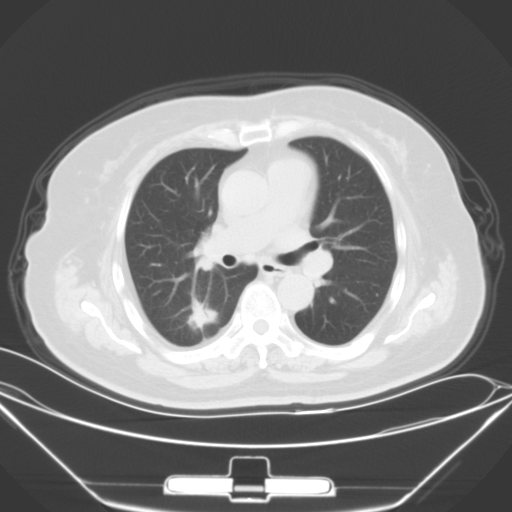
Chest CT, one axial slice; position 37 of 64 along the scan axis; 120 kVp; lung window (W 1500 / L -600 HU); 512 × 512 image matrix. Patient: female, 70 years. Case-level facts recorded for this patient, not image findings: clinical TNM (as recorded): T2 N0 M3.
Outlined on this slice (bounding box drawn by a radiologist):
- lung tumour (recorded histology: adenocarcinoma): bounding box [x1, y1, x2, y2] px = [180, 296, 222, 339]